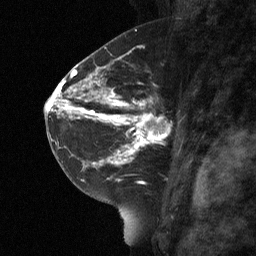
Breast MRI (dynamic contrast-enhanced), one sagittal slice. Slice 36 of 64 in the series (ordered by position). Dynamic contrast-enhanced study with each time point stored as its own series, time point 2 of 3 at this slice position (early post-contrast, ordered by acquisition time). 1.5 T. TE 4.8 ms, TR 27 ms. 2 mm slice thickness. 256 × 256 image matrix. Patient: female, 42 years. From the clinical record (not read from this slice): setting: breast cancer imaged before/during neoadjuvant chemotherapy; receptor status: triple-negative.
Outlined on this slice (semi-automatically segmented with operator editing):
- analysis volume of interest (the breast-tissue region the enhancement analysis was run in; not a lesion): bounding box [x1, y1, x2, y2] px = [115, 85, 183, 160]
- tumour enhancement mask (voxels above the 90 % enhancement threshold inside the analysis volume of interest): [115, 95, 161, 160]